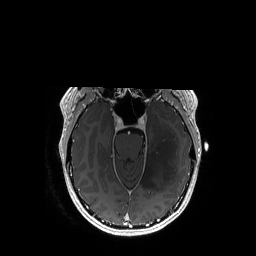
Brain MRI from a brain-tumour surgery series, one axial slice. Position 114 of 192 along the scan axis. T1-weighted post-contrast. 1 mm slice thickness. 256 × 256 image matrix, field of view 256 × 256 mm. Case-level facts recorded for this patient, not image findings: histopathology: Astrocytoma; WHO grade: 3; IDH mutation: yes; tumour location: Left Temporal.
Annotated regions visible in this slice (outlined manually by an expert reader):
- tumour: bounding box (x1, y1, x2, y2) in pixels: (141, 115, 178, 190)